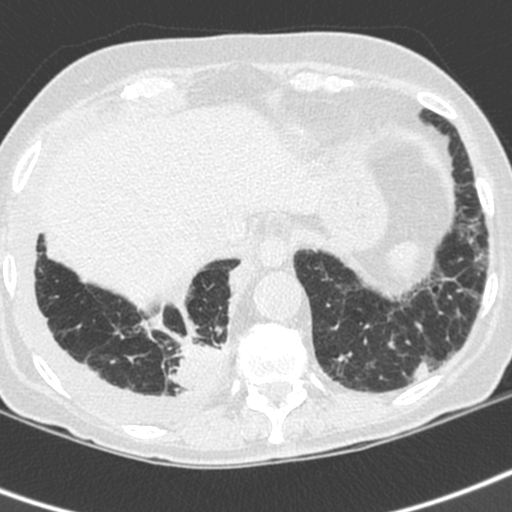
Chest CT (low-dose screening protocol), one axial image, first (baseline) screen, lung window (W 1500 / L -600 HU), 1.3 mm slice thickness, standard (soft-tissue) reconstruction kernel (C), slice 155 of 192 in the series, 512 × 512 image matrix, field of view 288 × 288 mm. Female participant, aged 73 years at enrolment. Current smoker at enrolment.
Expert reader's lesion annotation, bounding box <160,326,235,405> (left, top, right, bottom; pixels). Screening reader's record for this exam (one nodule recorded; not confirmed to be the boxed lesion): non-calcified nodule or mass ≥4 mm, right lower lobe, 35 × 30 mm, spiculated (stellate) margins, soft tissue attenuation. Participant outcome: lung cancer diagnosed 22 days after this screen — adenocarcinoma, NOS, right lower lobe, stage IV (AJCC 6th edition), 35 mm at pathology.